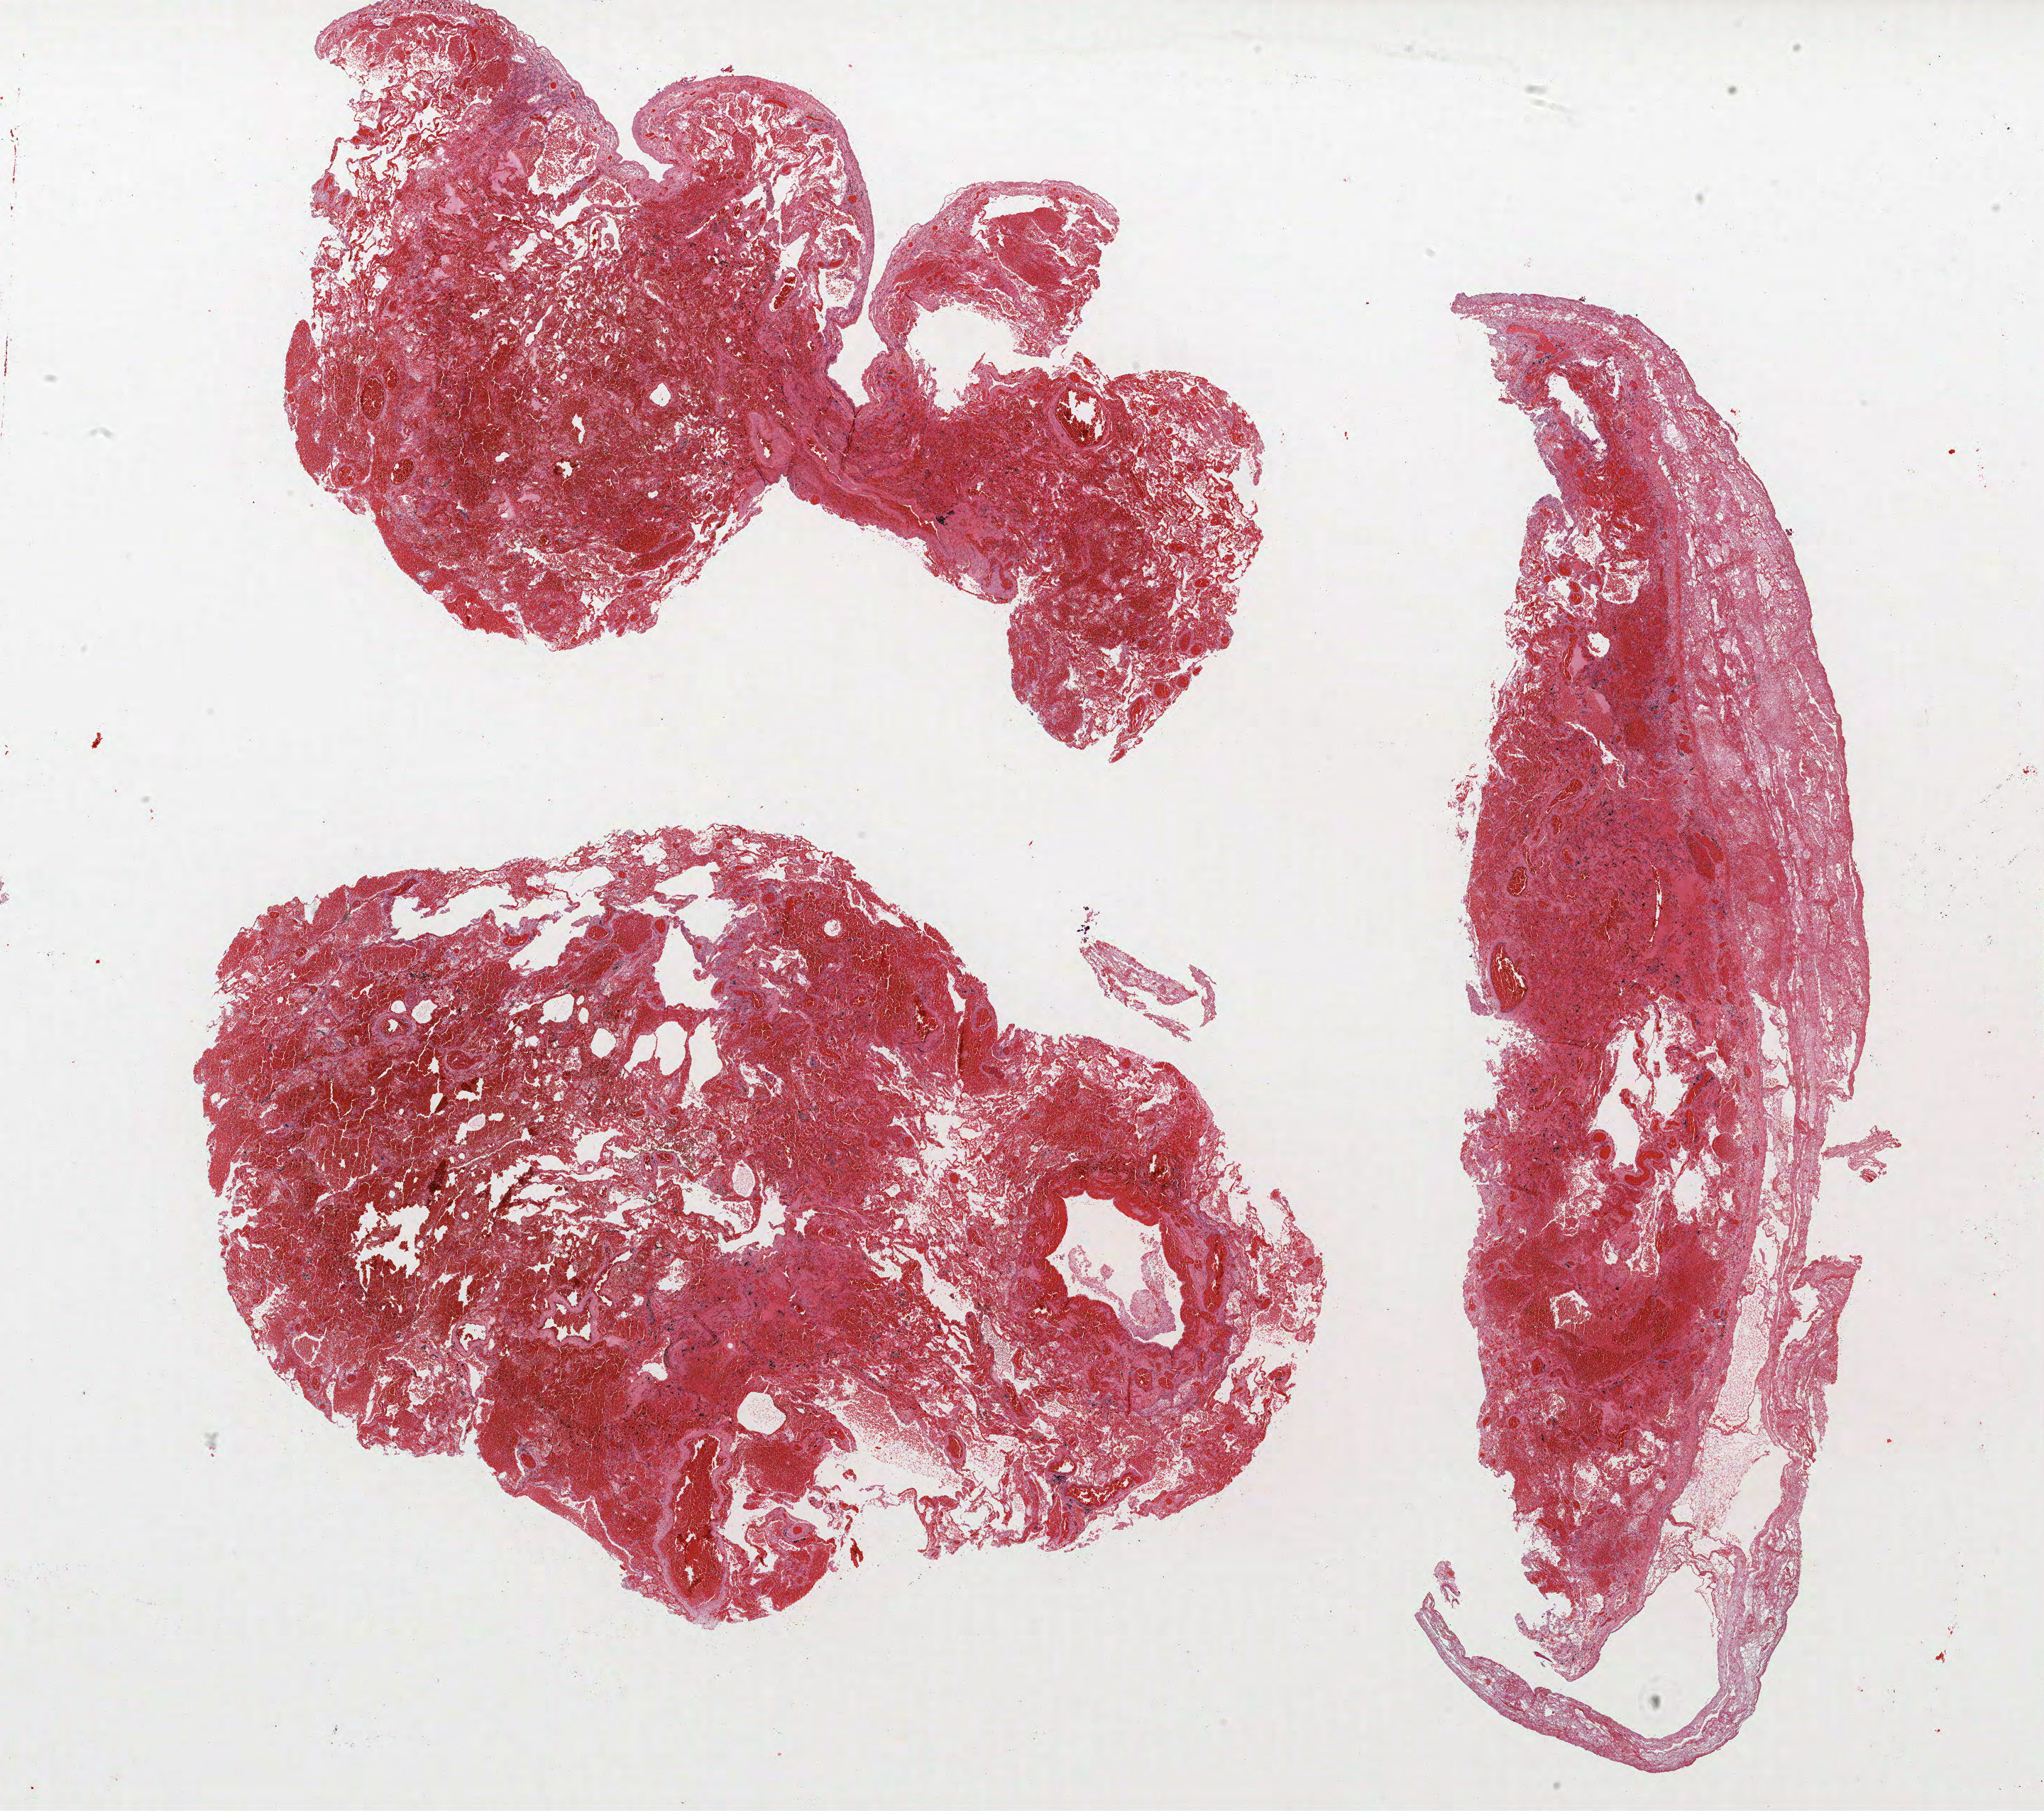
Hematoxylin and eosin (H&E) stained whole-slide image — shown as a low-resolution overview of the whole scanned area (about 23.0 x 20.4 mm, acquisition: 40x scan). FFPE section. Lung. Male, age 67 at enrolment. Current smoker at enrolment.
Tumour size (pathology): 20 mm. Stage (AJCC 6th edition): IA. Primary tumour location (clinical record): right middle lobe. Participant's lung-cancer diagnosis: Small cell carcinoma, NOS.